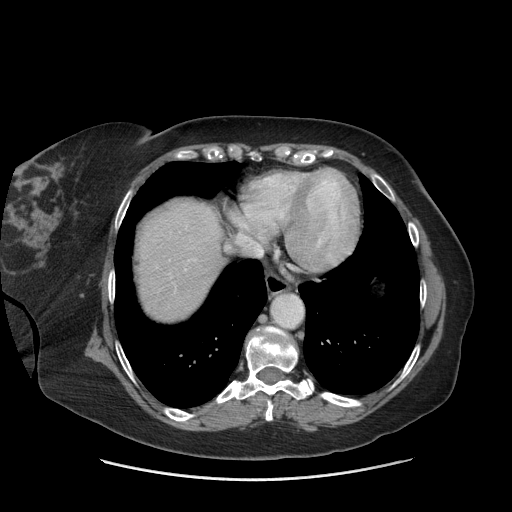
Contrast-enhanced abdominal CT (liver protocol), one axial slice. Slice 66 of 69 in the series (ordered by position). Reconstruction kernel STANDARD. Soft-tissue window (W 400 / L 40 HU). 2.5 mm slice thickness. 512 × 512 image matrix, field of view 420 × 420 mm. Case-level facts recorded for this patient, not image findings: diagnosis: hepatocellular carcinoma (patient treated with transarterial chemoembolisation; whether this scan precedes or follows treatment is not stated here); TNM stage (as recorded): Stage-IIIB; Child-Pugh class: A; tumour differentiation: moderately differentiated.
Annotated regions visible in this slice (semi-automatically segmented with operator editing):
- abdominal aorta: box from (x=271, y=295) to (x=302, y=327) px
- liver parenchyma outside the tumour (the mass and vessels are separate outlines, so this box may not span the whole liver): (x=138, y=200)–(x=222, y=318)